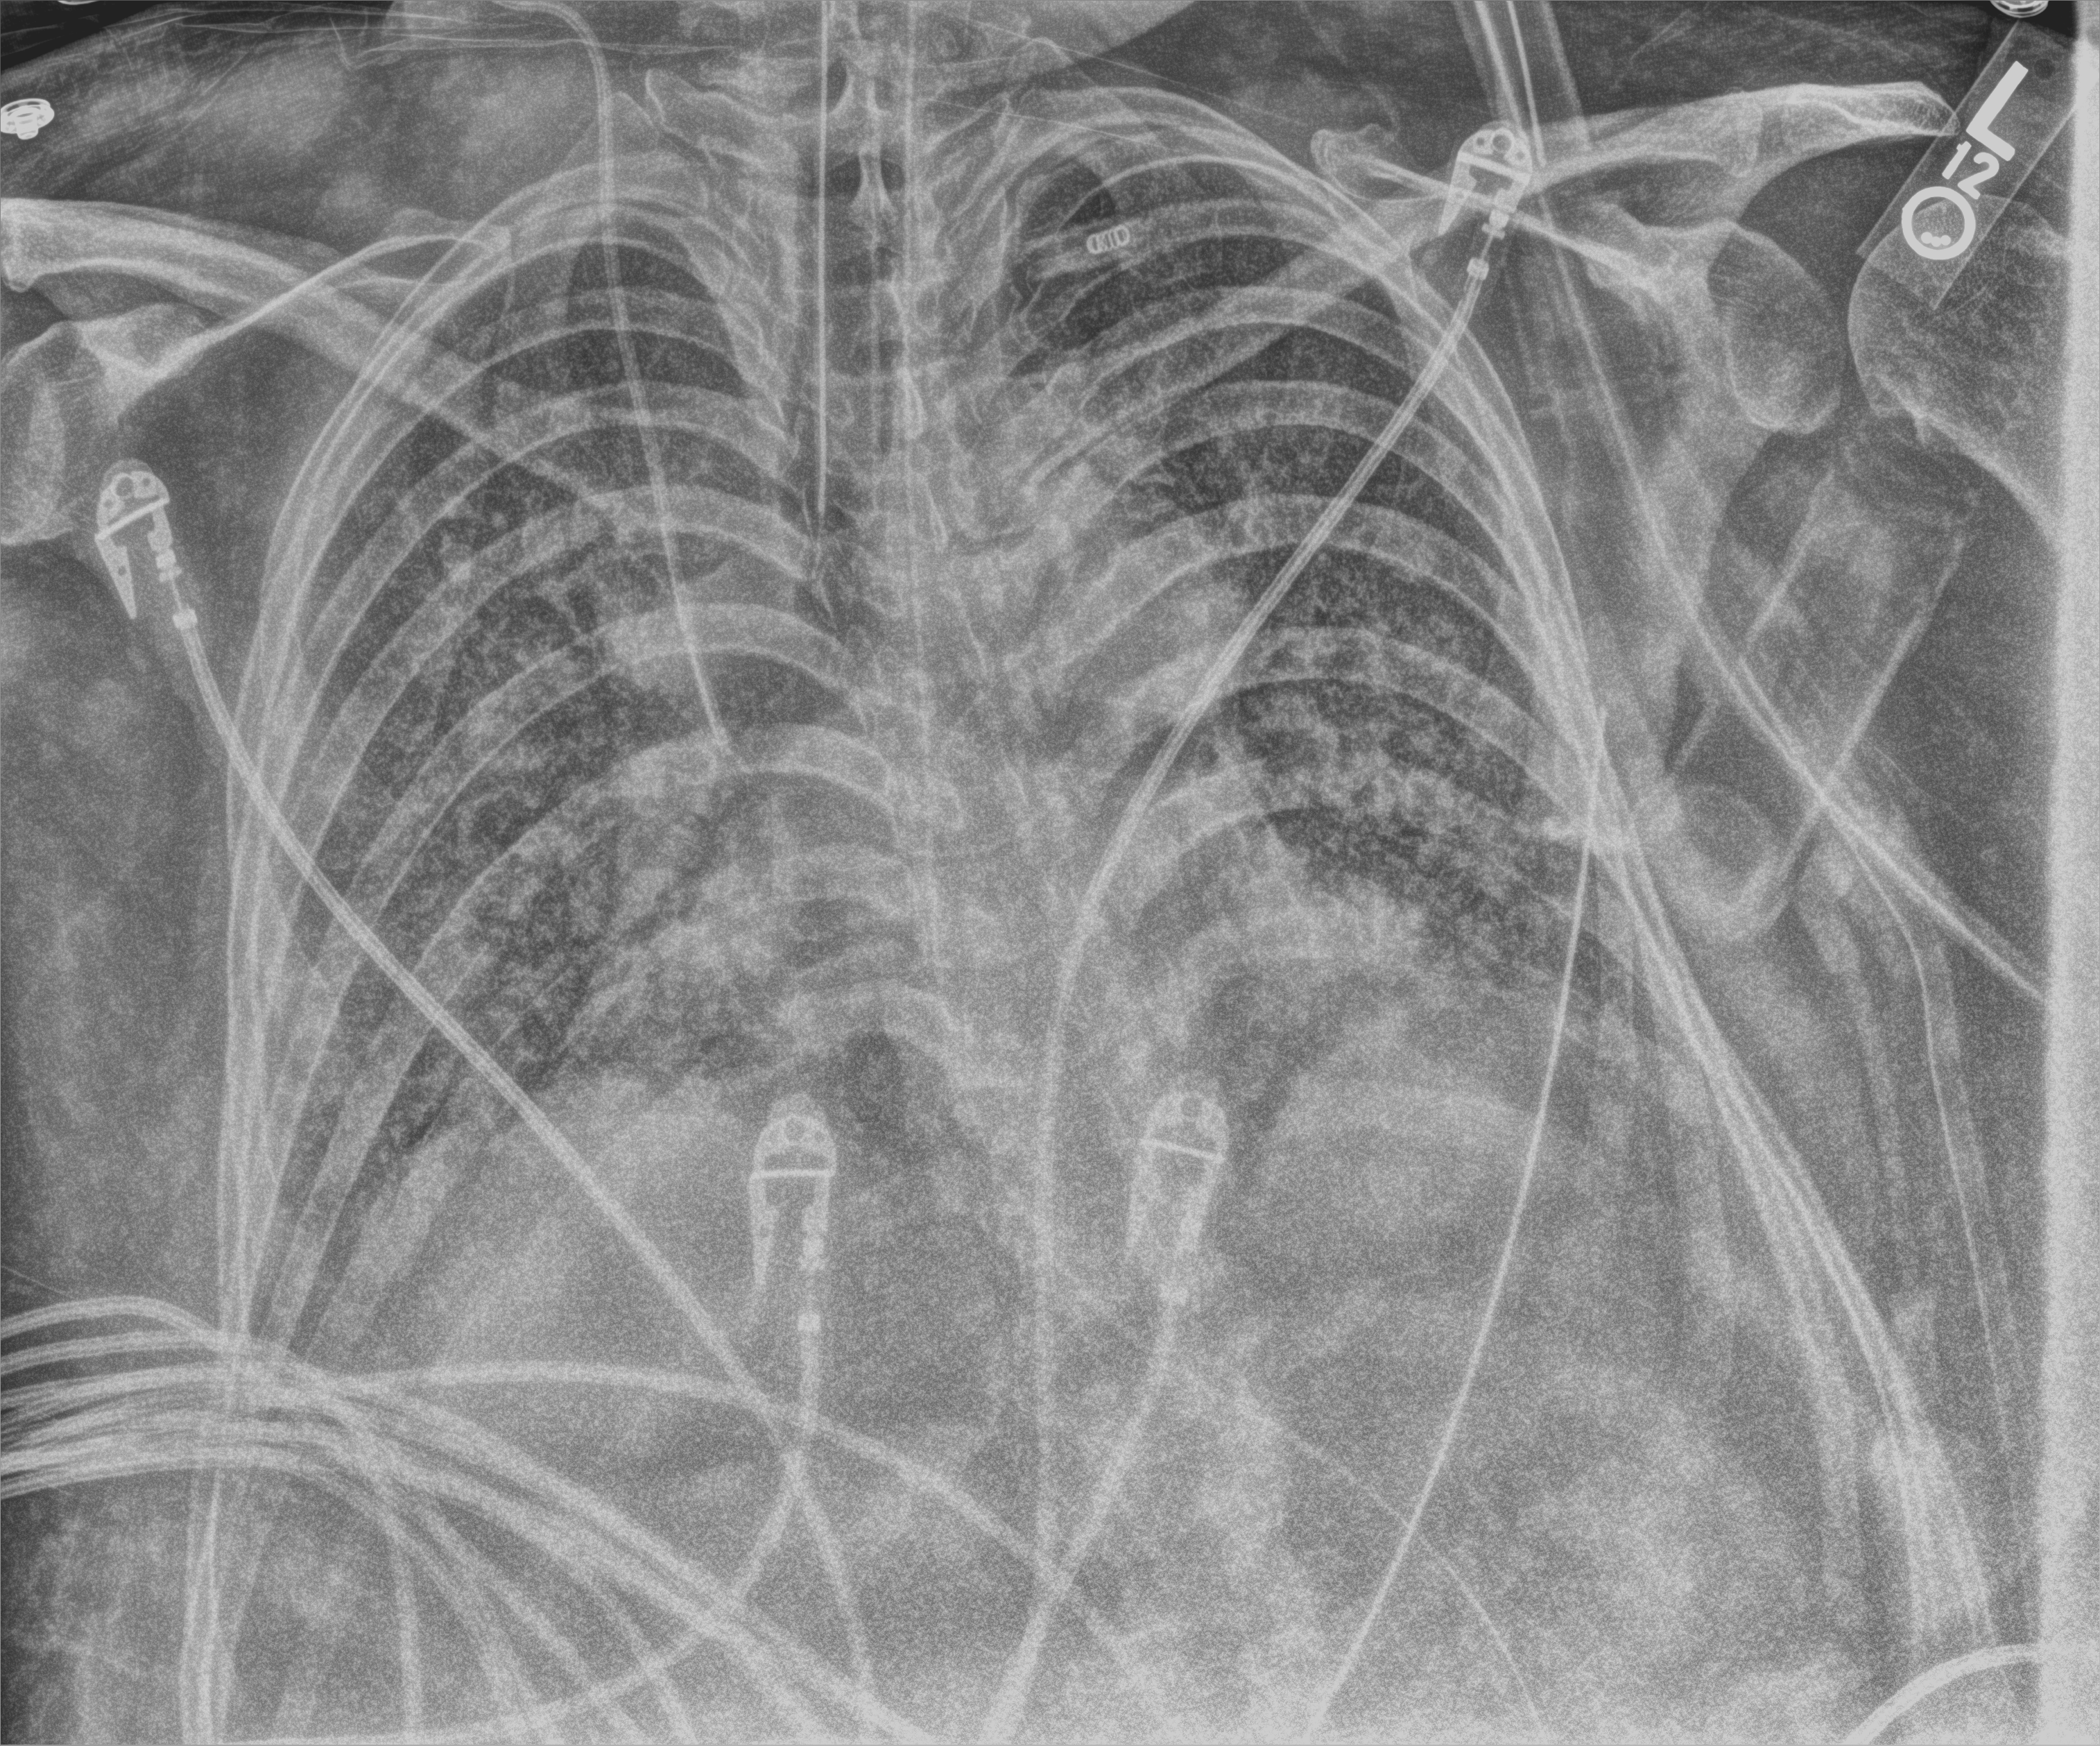
Portable chest radiograph, anteroposterior (AP) projection. Adult patient hospitalised with COVID-19, age 18–59 years.
From the hospital-stay record, not from the radiograph (when in the stay this image was taken is not recorded): mechanically ventilated during this hospital stay: yes.